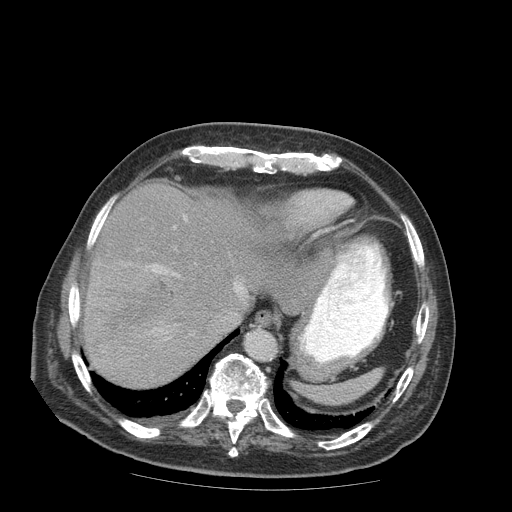
Contrast-enhanced abdominal CT (liver protocol), one axial slice; slice 71 of 99 in the series (ordered by position); reconstruction kernel STANDARD; 140 kVp; soft-tissue window (W 400 / L 40 HU); 2.5 mm slice thickness; 512 × 512 image matrix, field of view 420 × 420 mm. Case-level facts recorded for this patient, not image findings: diagnosis: hepatocellular carcinoma (patient treated with transarterial chemoembolisation; whether this scan precedes or follows treatment is not stated here); TNM stage (as recorded): Stage-IIIB; Child-Pugh class: A; tumour differentiation: well differentiated.
Structures marked on this image (semi-automatically segmented with operator editing):
- liver parenchyma outside the tumour (the mass and vessels are separate outlines, so this box may not span the whole liver): box from (x=84, y=182) to (x=297, y=386) px
- mass: (x=102, y=264)–(x=176, y=337)
- liver vessels: (x=146, y=216)–(x=244, y=340)